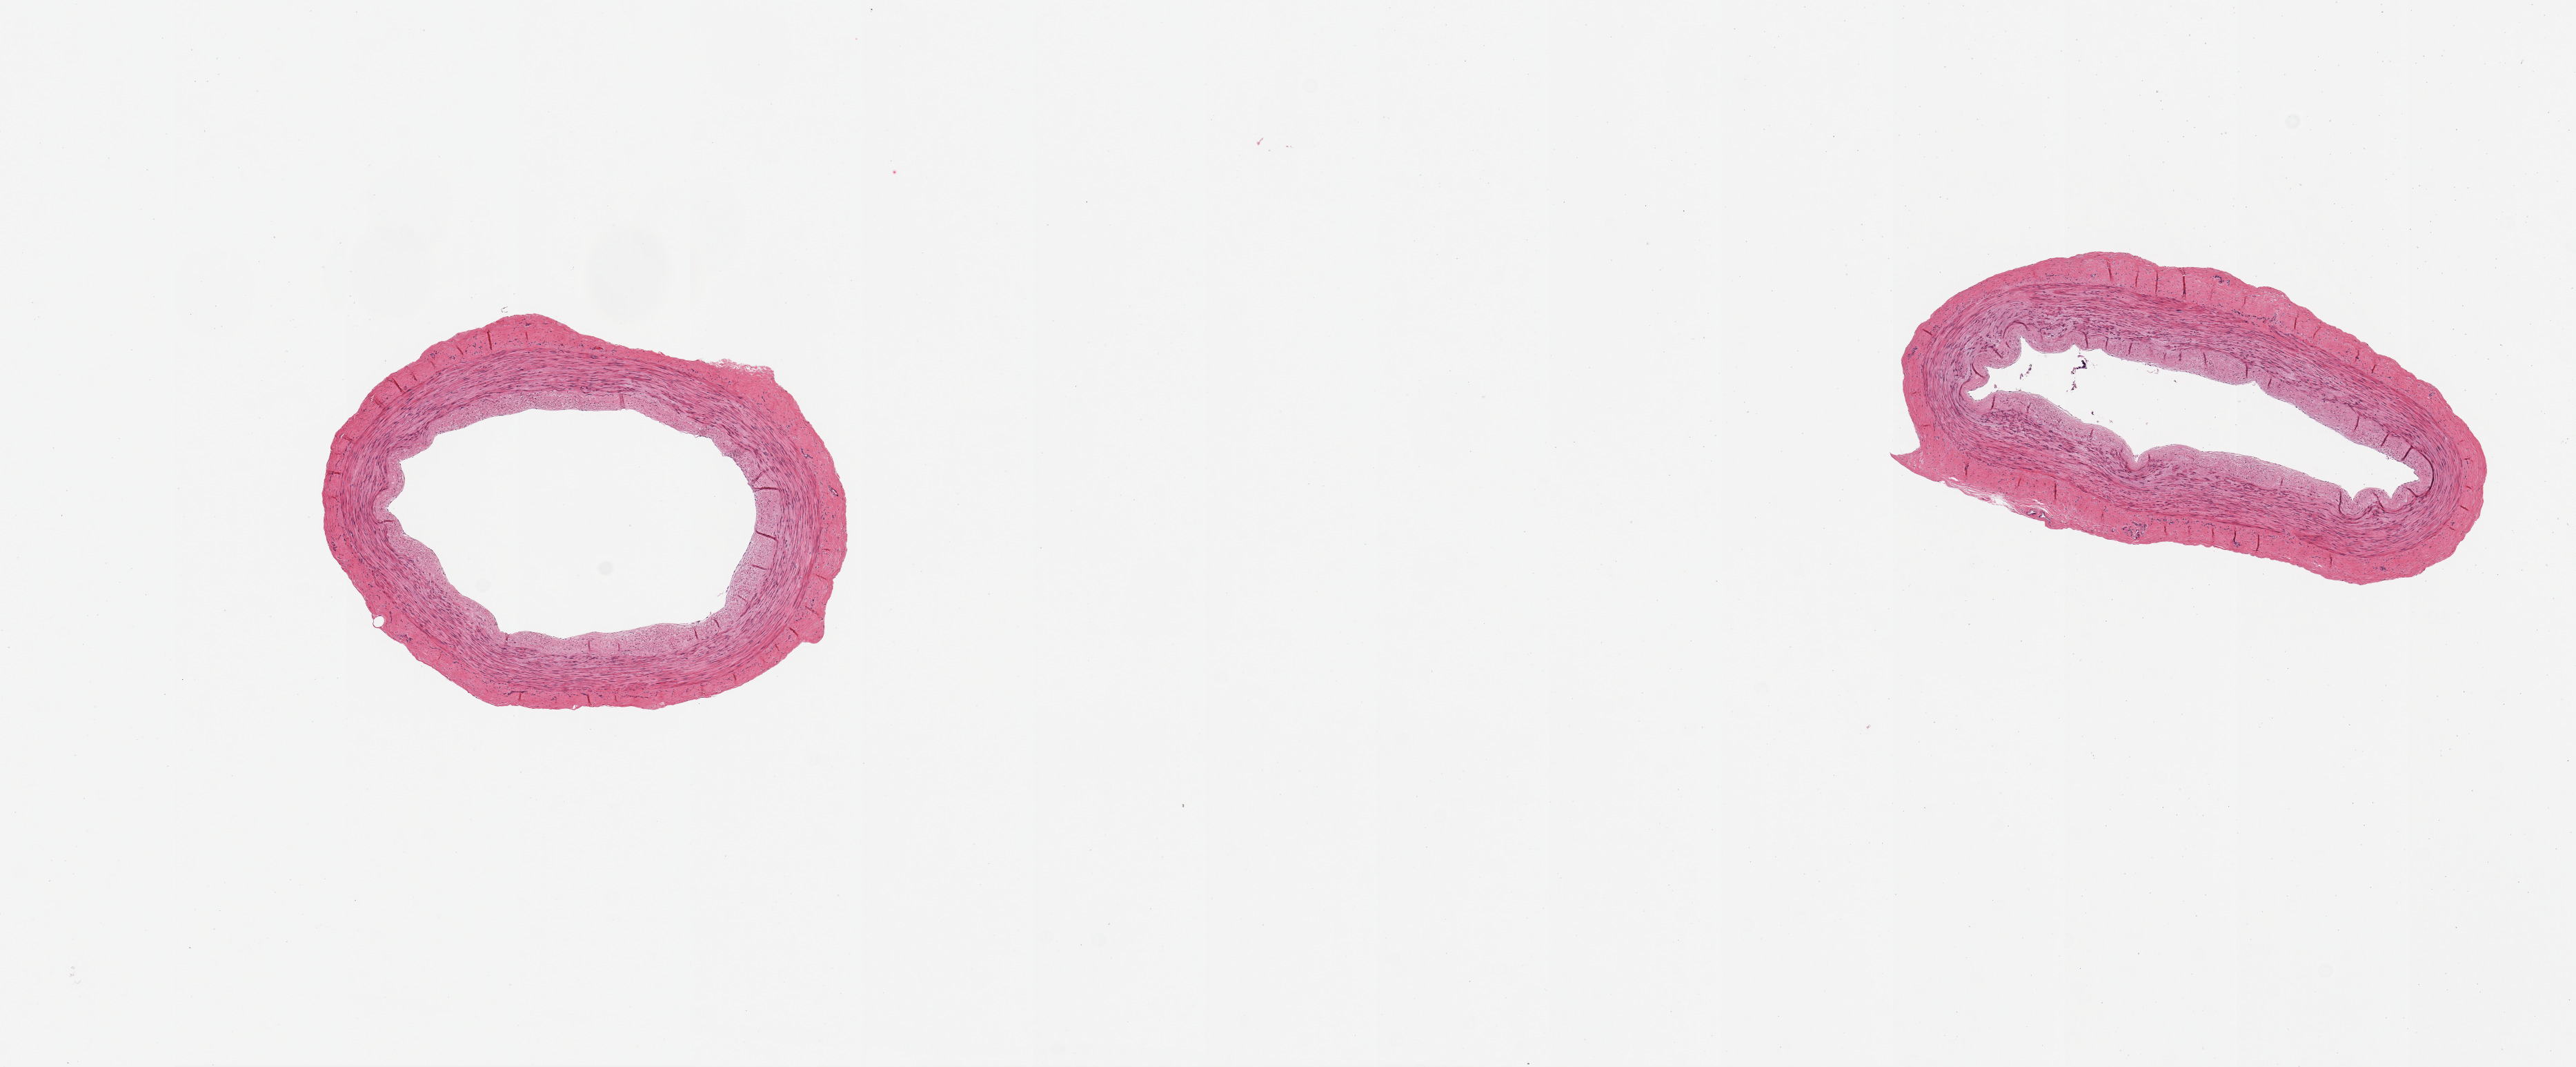
Whole-slide image, haematoxylin and eosin stain, low-resolution overview of the scanned area, about 14.8 x 6.1 mm; PAXgene-fixed paraffin-embedded (PFPE) section; section of tibial artery (target tissue); donor tissue sample. Male donor.
Review note (as recorded): 2 pieces, no atherosis, clean specimens.